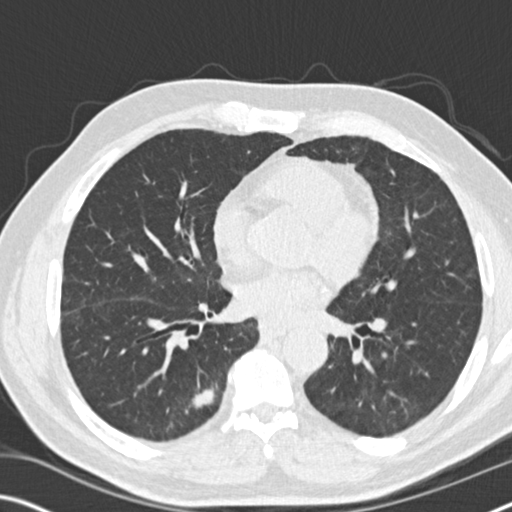
Low-dose screening chest CT, one axial slice; position 80 of 169 along the scan axis; 120 kVp; lung window (W 1500 / L -600 HU); 2 mm slice thickness; 512 × 512 image matrix, field of view 340 × 340 mm.
Structures marked on this image (manually delineated by an expert):
- lesion 1 (tumor, lower lobe of right lung): bounding box <193,387,215,409> (left, top, right, bottom; pixels)